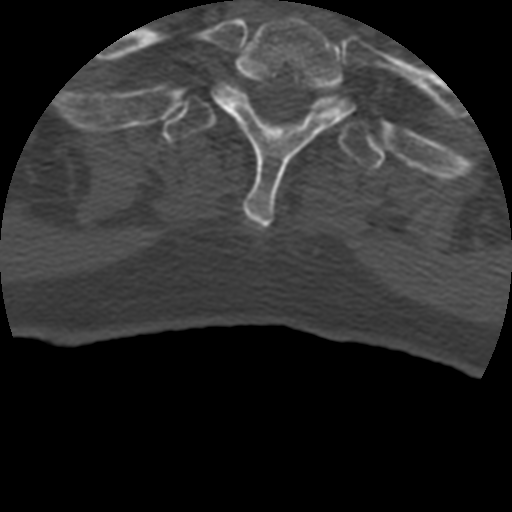
CT including the spine, one axial slice; slice 379 of 399 in the series (ordered by position); reconstruction kernel STANDARD; bone window (W 1800 / L 400 HU); 1.25 mm slice thickness; 512 × 512 image matrix. Patient age 69 years. From the clinical record (not read from this slice): primary cancer: prostate.
Structures marked on this image (semi-automatic segmentation, software-assisted and operator-edited):
- T1 vertebra: bounding box [x1, y1, x2, y2] px = [209, 17, 354, 229]
- T2 vertebra: [162, 83, 386, 170]